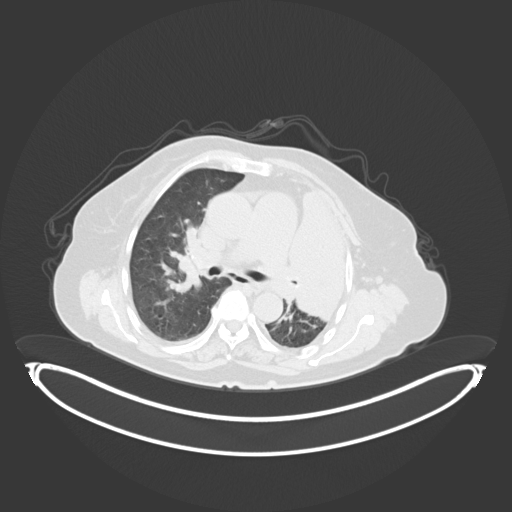
Chest CT, one axial slice; slice 206 of 284 in the series (ordered by position); reconstruction kernel B30f; lung window (W 1500 / L -600 HU); 3 mm slice thickness; 512 × 512 image matrix, field of view 500 × 500 mm. Patient: female, 75 years. From the clinical record (not read from this slice): clinical TNM (as recorded): T3 N3 M1.
Structures marked on this image (bounding box drawn by a radiologist):
- lung tumour (recorded histology: adenocarcinoma): box from (x=282, y=185) to (x=357, y=324) px